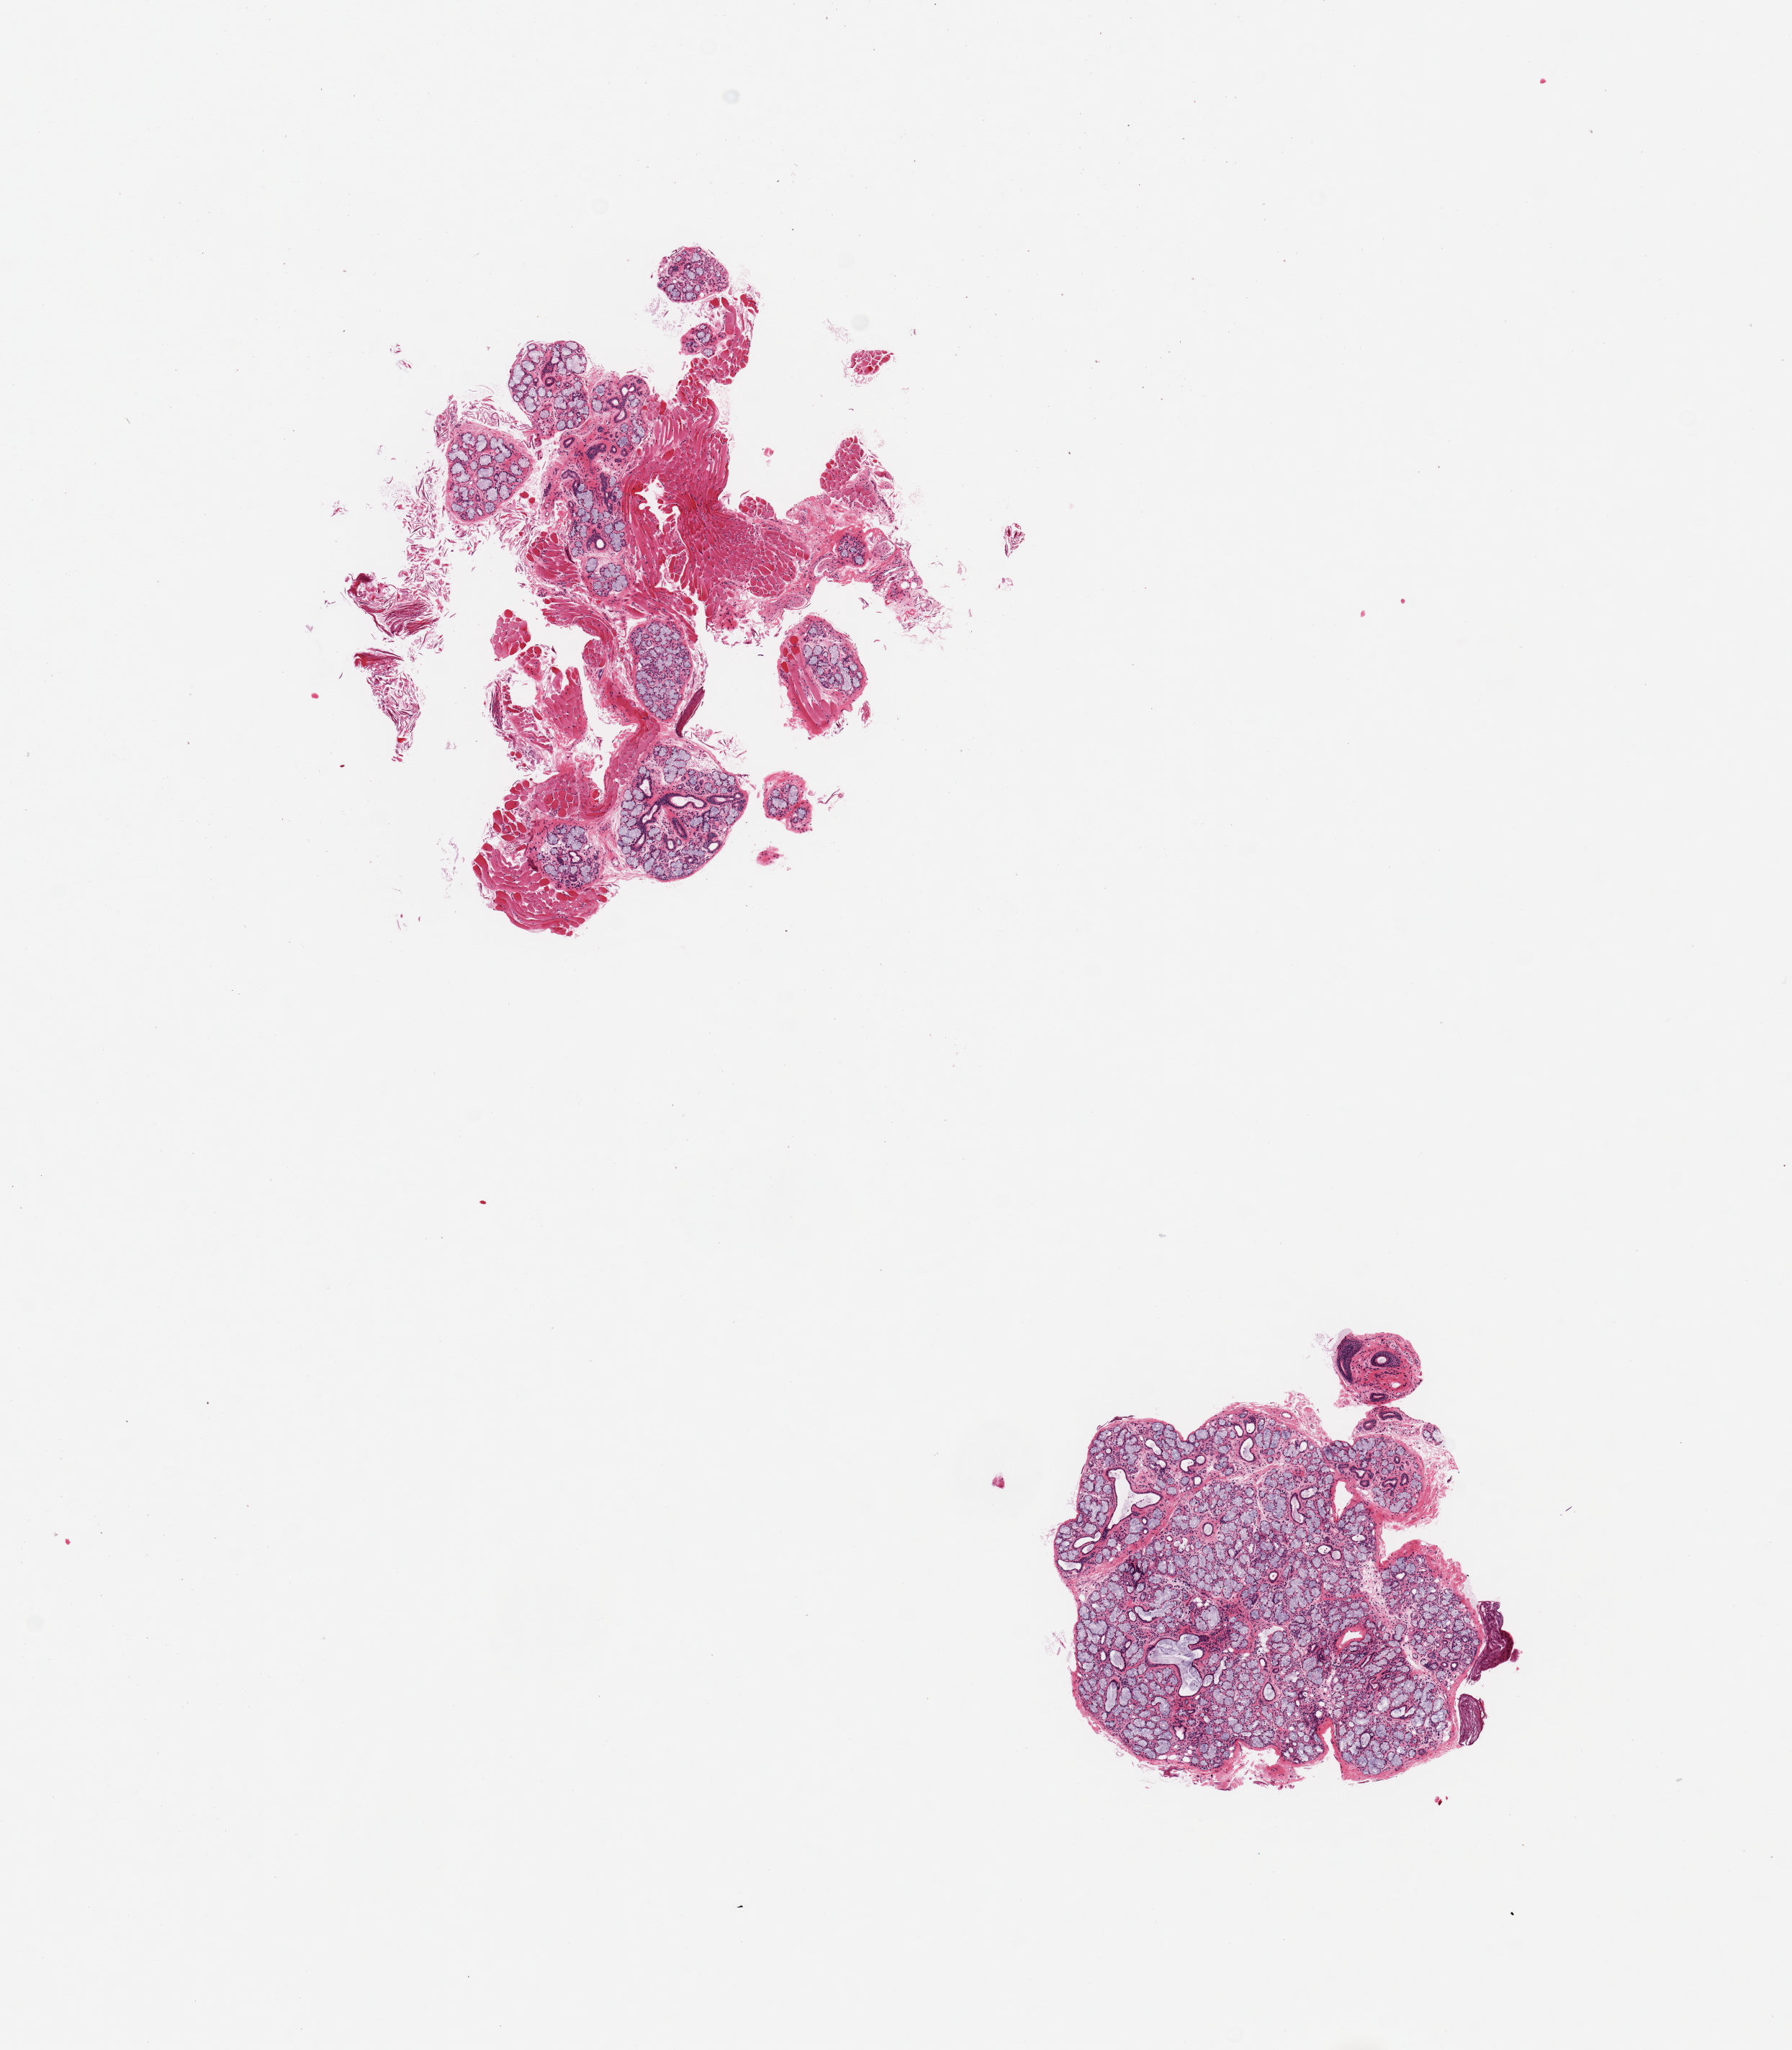
Digitized hematoxylin and eosin (H&E)-stained section, low-resolution overview of the scanned area, about 9.8 x 11.3 mm, PAXgene-fixed paraffin-embedded (PFPE) section, section of minor salivary gland (target tissue), tissue donor sample. Donor: male.
Pathologist's review note for this sample: 2 pieces, ~70% glandular parenchyma.